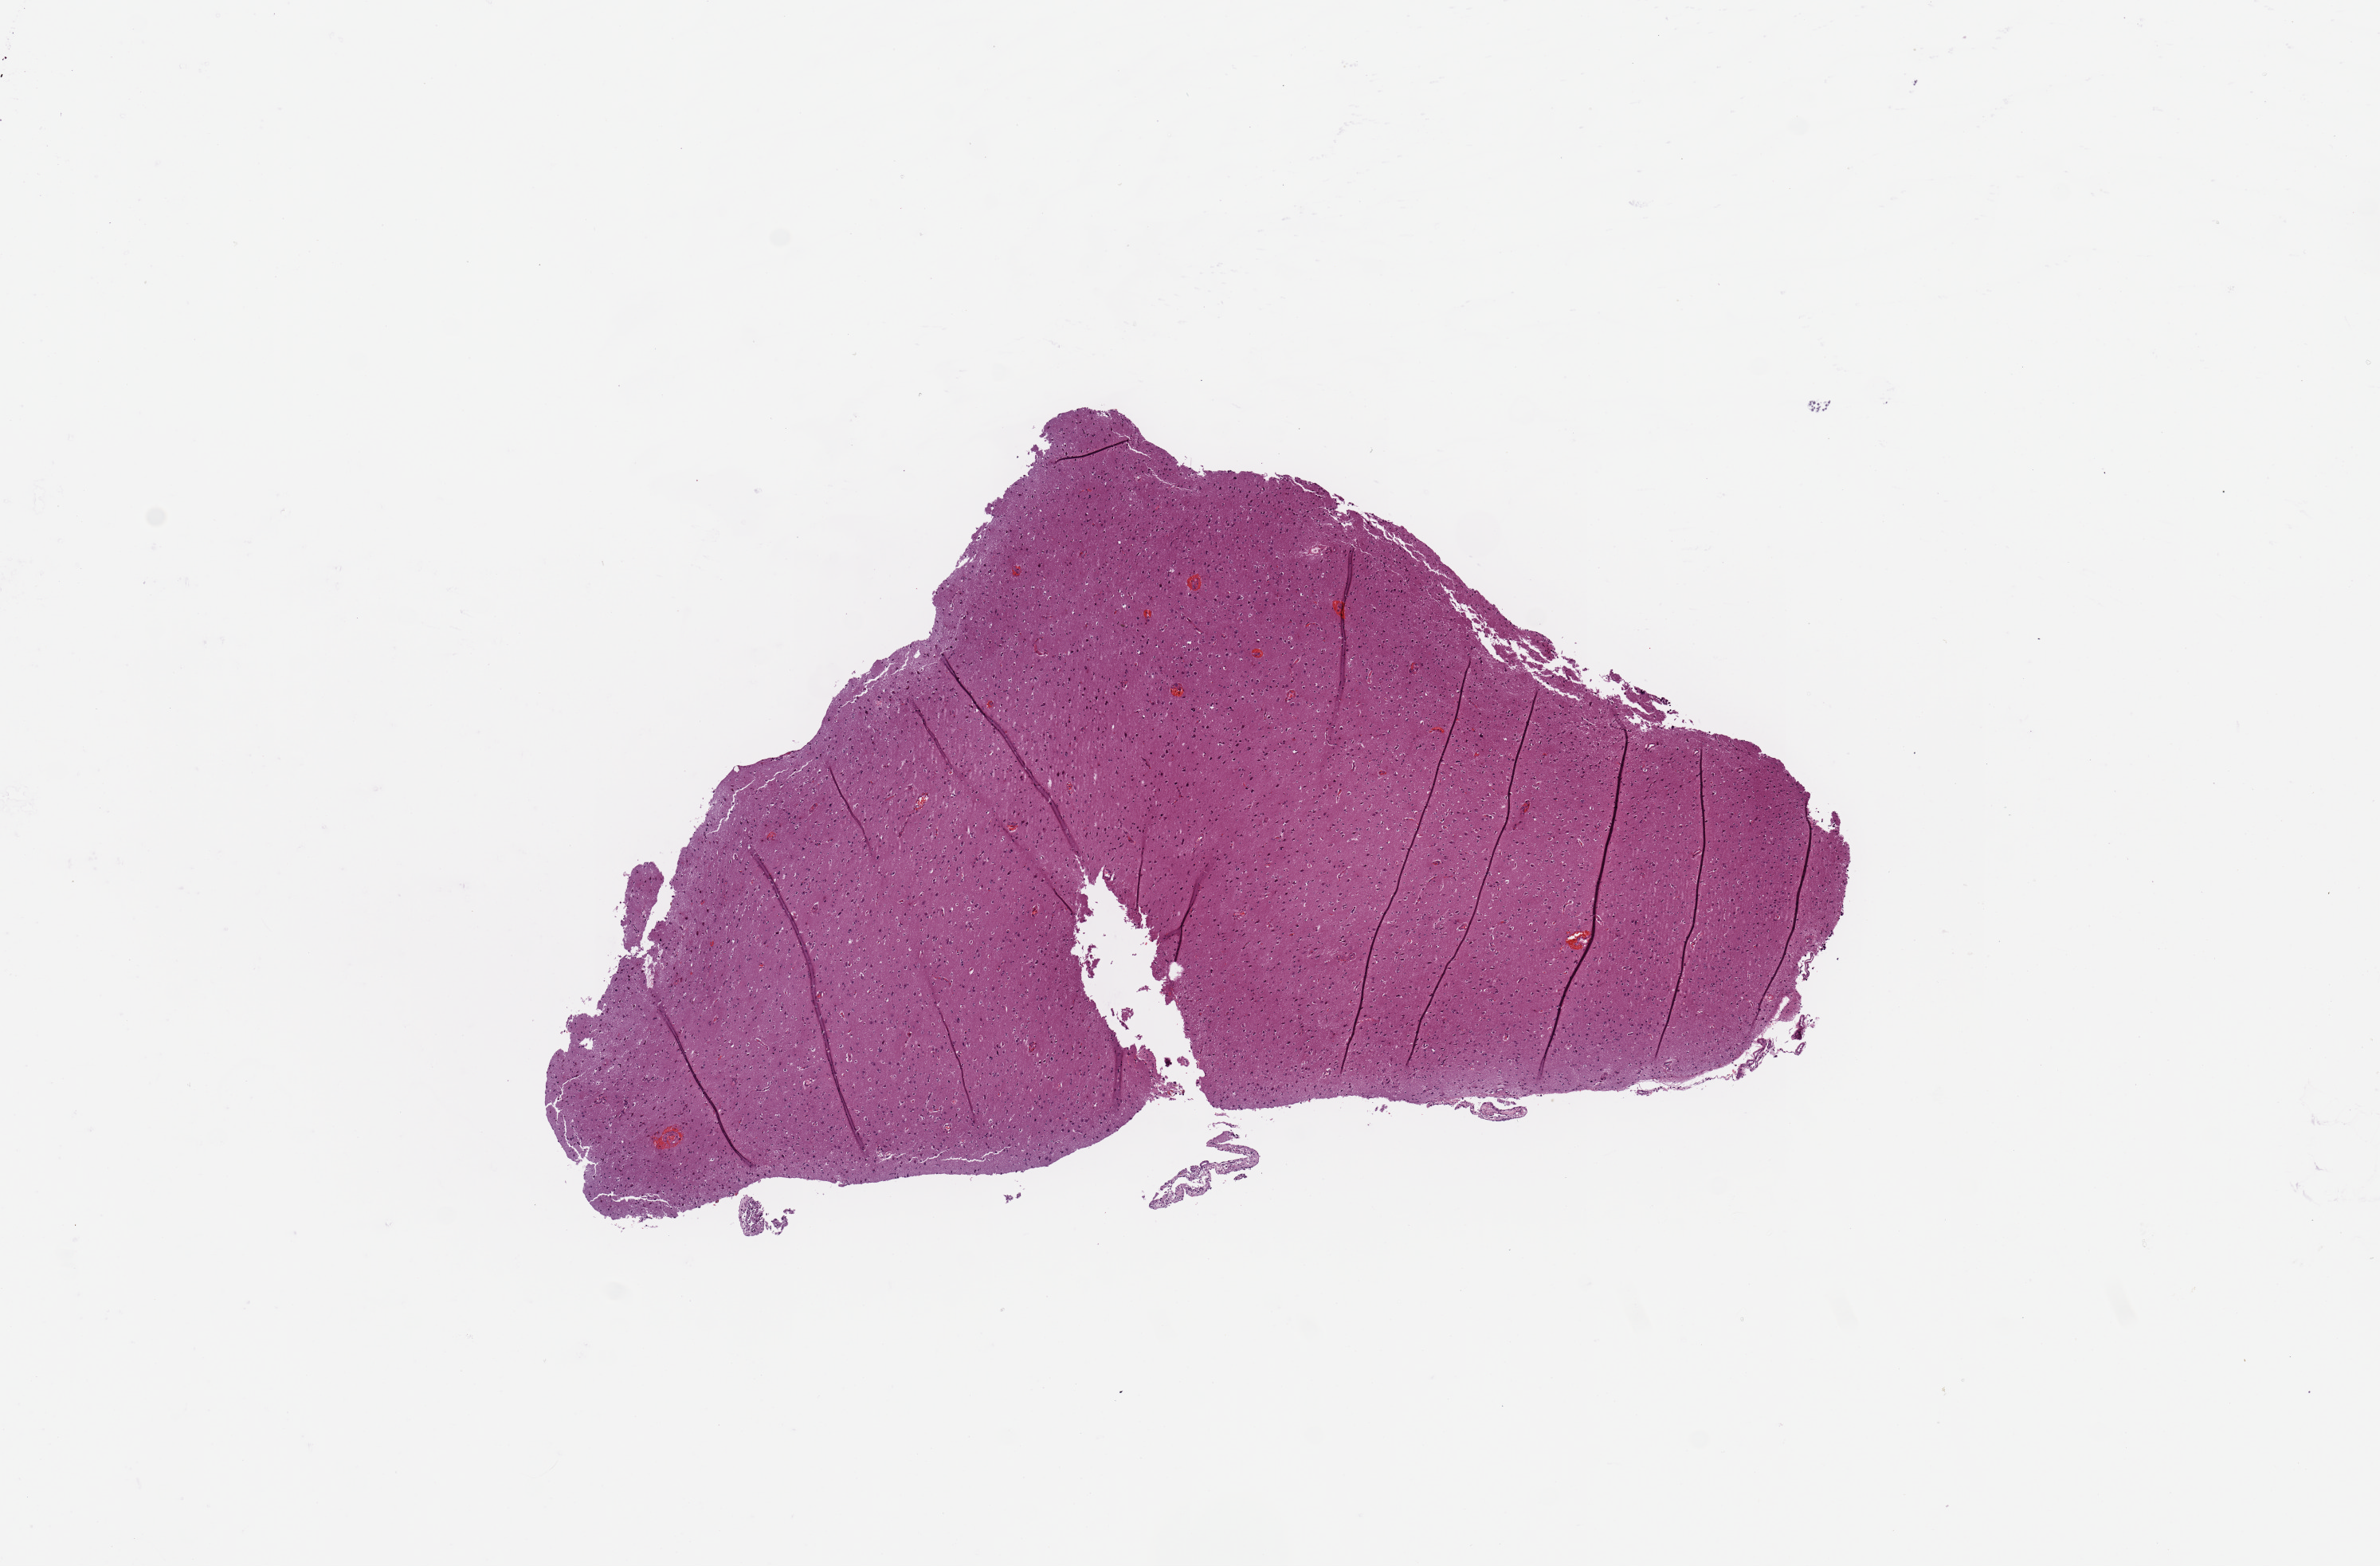
Whole-slide histology image, Hematoxylin and eosin (H&E) stained, shown as a low-resolution overview of the whole scanned area (about 11.8 x 7.8 mm, acquisition: 20x scan); tumour tissue sample, brain. Patient: male, age 43 years.
Patient diagnosis (cohort enrolment): glioblastoma multiforme (brain).